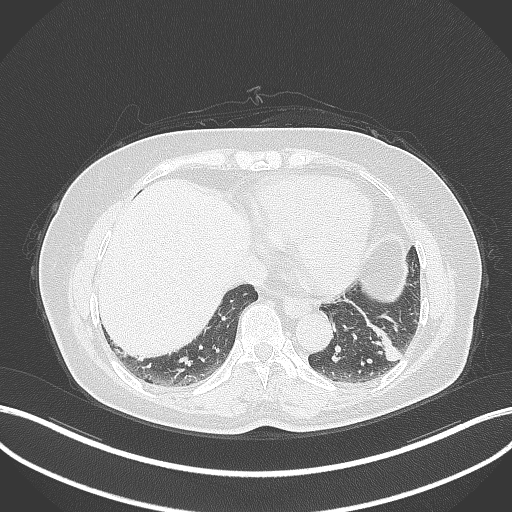
Chest CT, one axial slice. Lung window (W 1500 / L -600 HU). 1 mm slice thickness. 512 × 512 image matrix, field of view 400 × 400 mm. Patient: female, 59 years. Case-level facts recorded for this patient, not image findings: clinical TNM (as recorded): T2a N0 M0.
Outlined on this slice (bounding box drawn by a radiologist):
- lung tumour (recorded histology: adenocarcinoma): bounding box (x1, y1, x2, y2) in pixels: (367, 322, 402, 361)